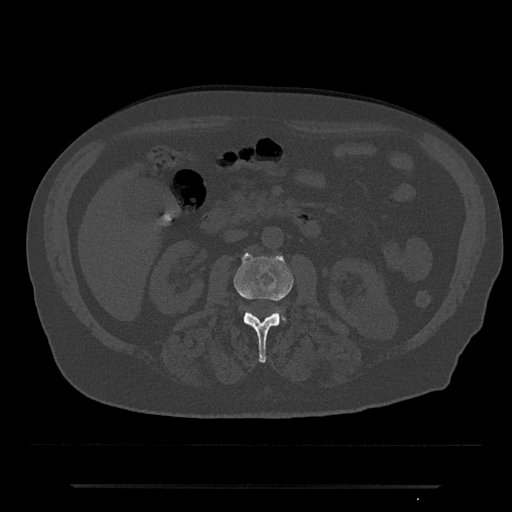
CT including the spine, one axial slice; reconstruction kernel Br40s/3; 120 kVp; bone window (W 1800 / L 400 HU); 0.5 mm slice thickness; 512 × 512 image matrix, field of view 434 × 434 mm. Male patient, age 80 years. Case-level facts recorded for this patient, not image findings: primary cancer: prostate; vertebrae with lytic lesions (as recorded): L1, T11.
Outlined on this slice (semi-automatic segmentation, software-assisted and operator-edited):
- L2 vertebra: bounding box <233,253,294,363> (left, top, right, bottom; pixels)
- L3 vertebra: <282,316,286,322>